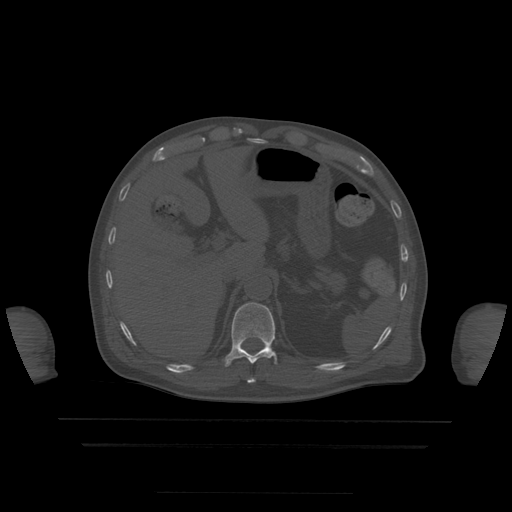
CT including the spine, one axial slice. Position 219 of 522 along the scan axis. Bone window (W 1800 / L 400 HU). 512 × 512 image matrix, field of view 436 × 436 mm. Patient age 68 years. Case-level facts recorded for this patient, not image findings: primary cancer: urothelial.
Annotated regions visible in this slice (semi-automatic segmentation, software-assisted and operator-edited):
- T10 vertebra: box from (x=248, y=379) to (x=255, y=384) px
- T11 vertebra: (x=225, y=303)–(x=277, y=367)